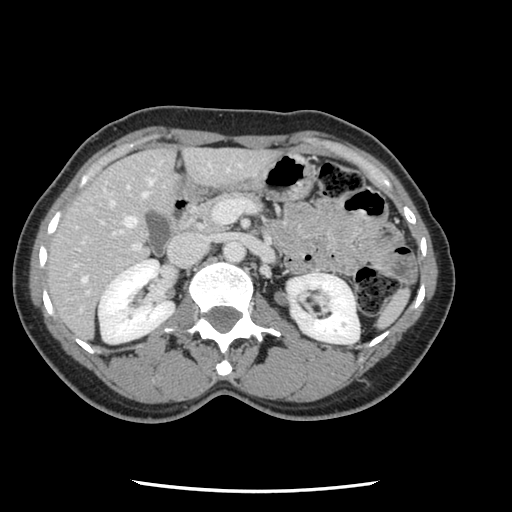
Contrast-enhanced abdominal CT, one axial slice. Slice 54 of 134 in the series (ordered by position). 120 kVp. Intravenous contrast given. Soft-tissue window (W 400 / L 40 HU). 2.5 mm slice thickness. 512 × 512 image matrix, field of view 330 × 330 mm. Female patient, age 43 years. Case-level facts recorded for this patient, not image findings: diagnosis: colorectal cancer liver metastases, imaged before liver resection; multiple liver metastases: yes; largest metastasis: 3.4 cm; disease in both lobes: yes.
Structures marked on this image (manually delineated by an expert):
- hepatic veins: bounding box (x1, y1, x2, y2) in pixels: (81, 177, 154, 284)
- liver: (47, 148, 273, 340)
- planned liver remnant (the part of the liver to remain after resection): (48, 148, 176, 330)
- portal vein (with intrahepatic branches): (68, 165, 255, 296)